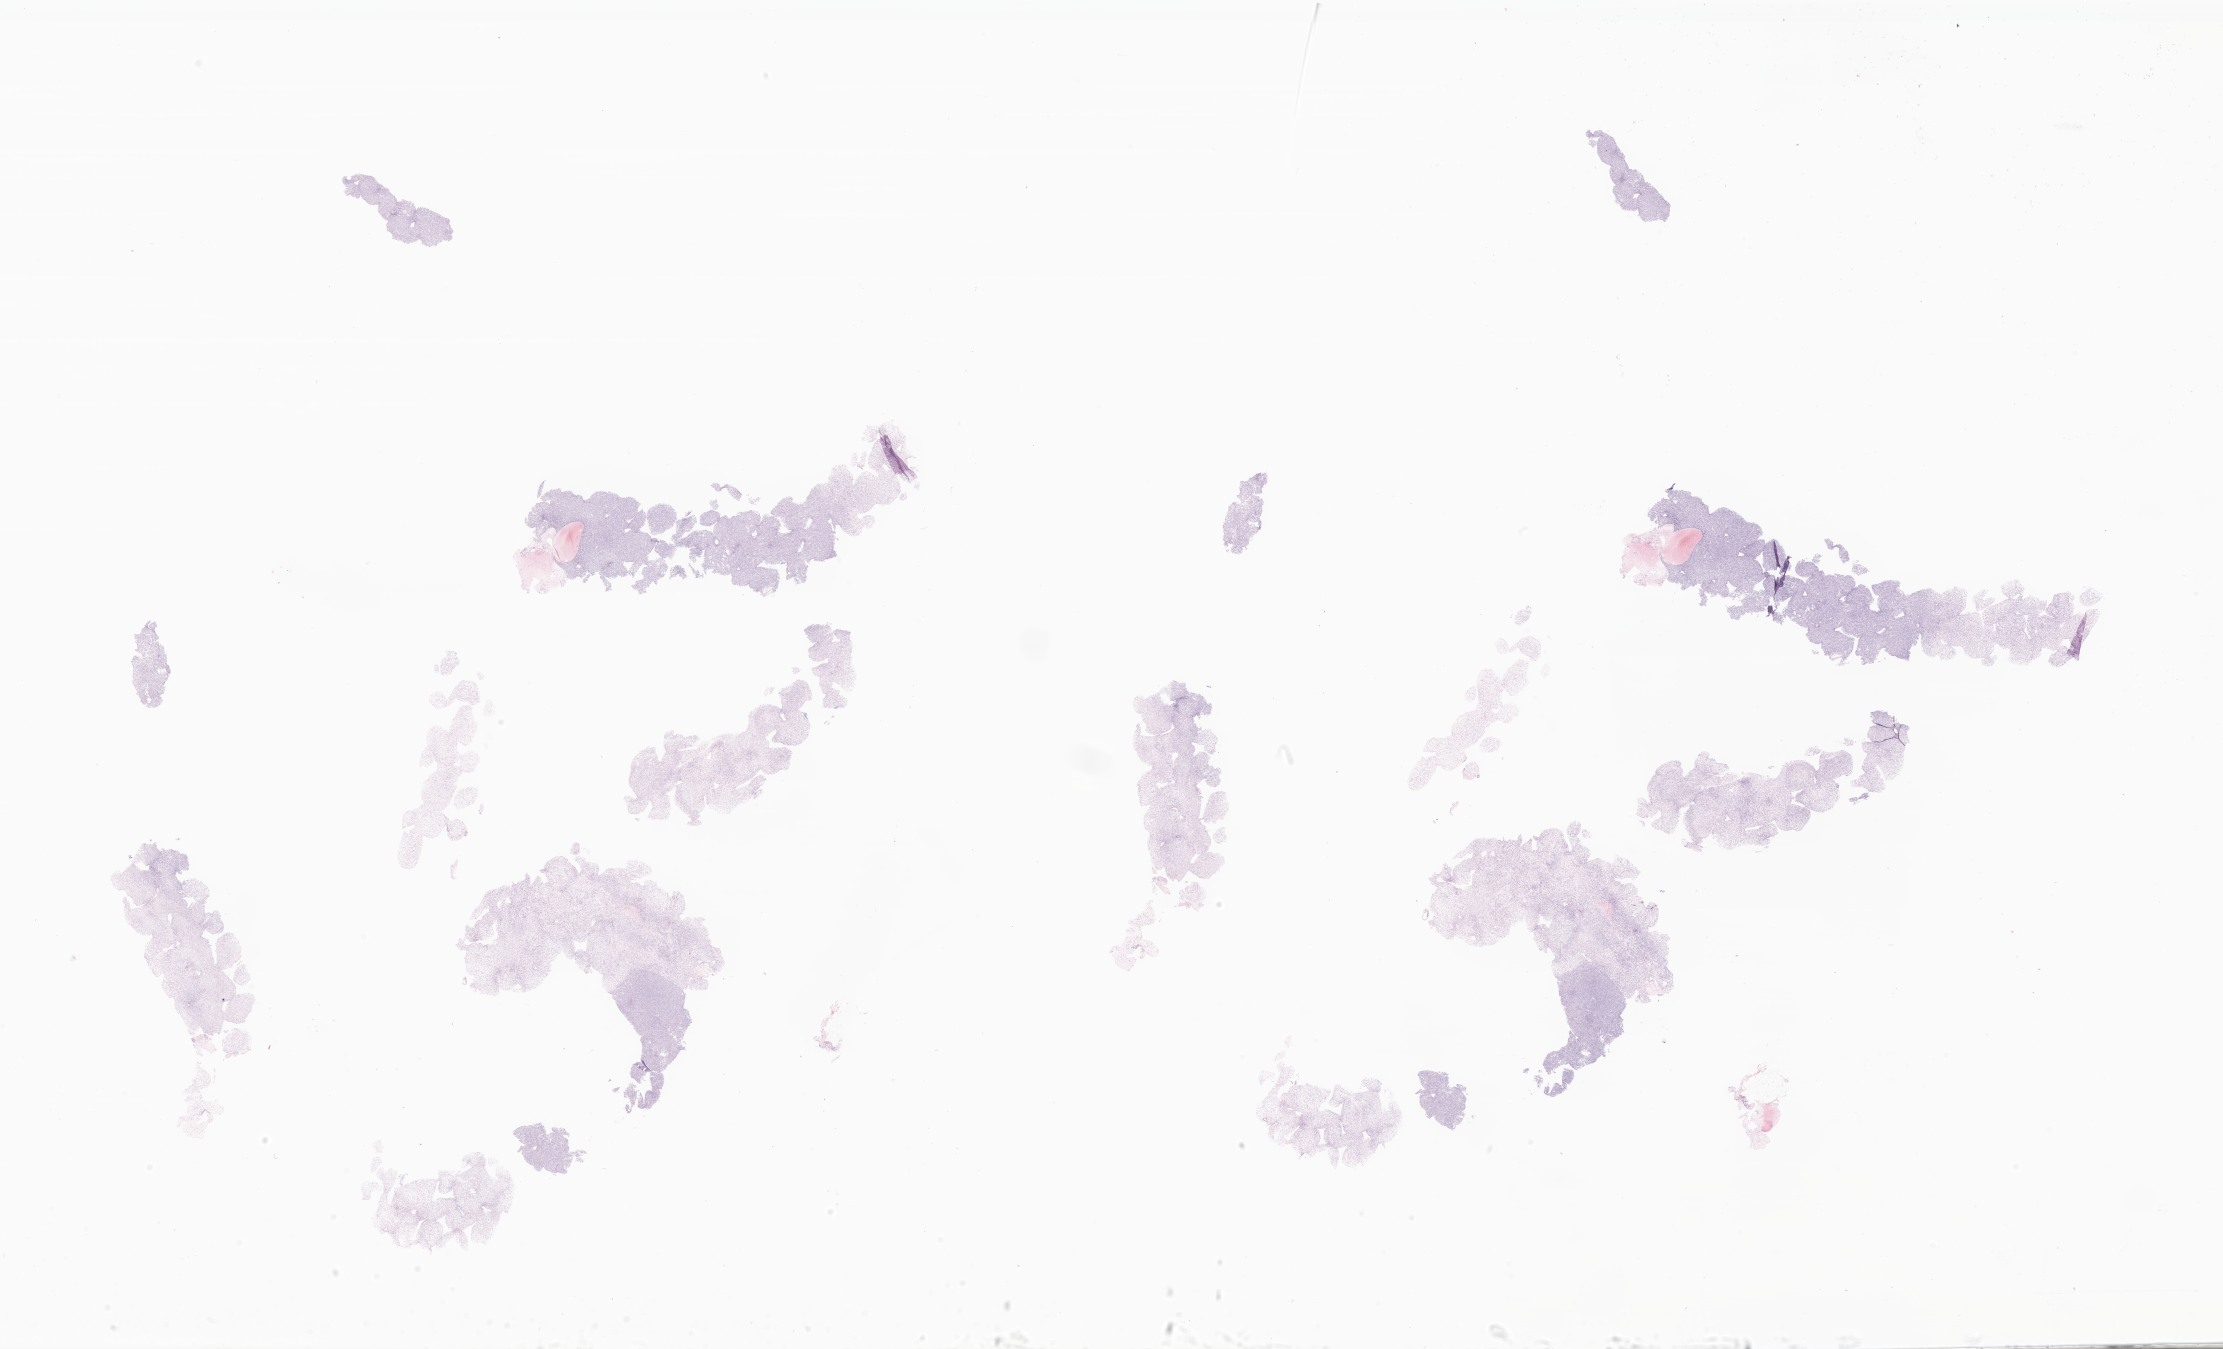
Digitized H&E-stained section of tumor tissue from the upper limb, shown as a low-resolution overview of the whole scanned area (about 37.5 x 22.8 mm), formalin-fixed paraffin-embedded section. Female patient, age 150 months (12 years 6 months).
• recorded diagnosis: Synovial sarcoma, spindle cell